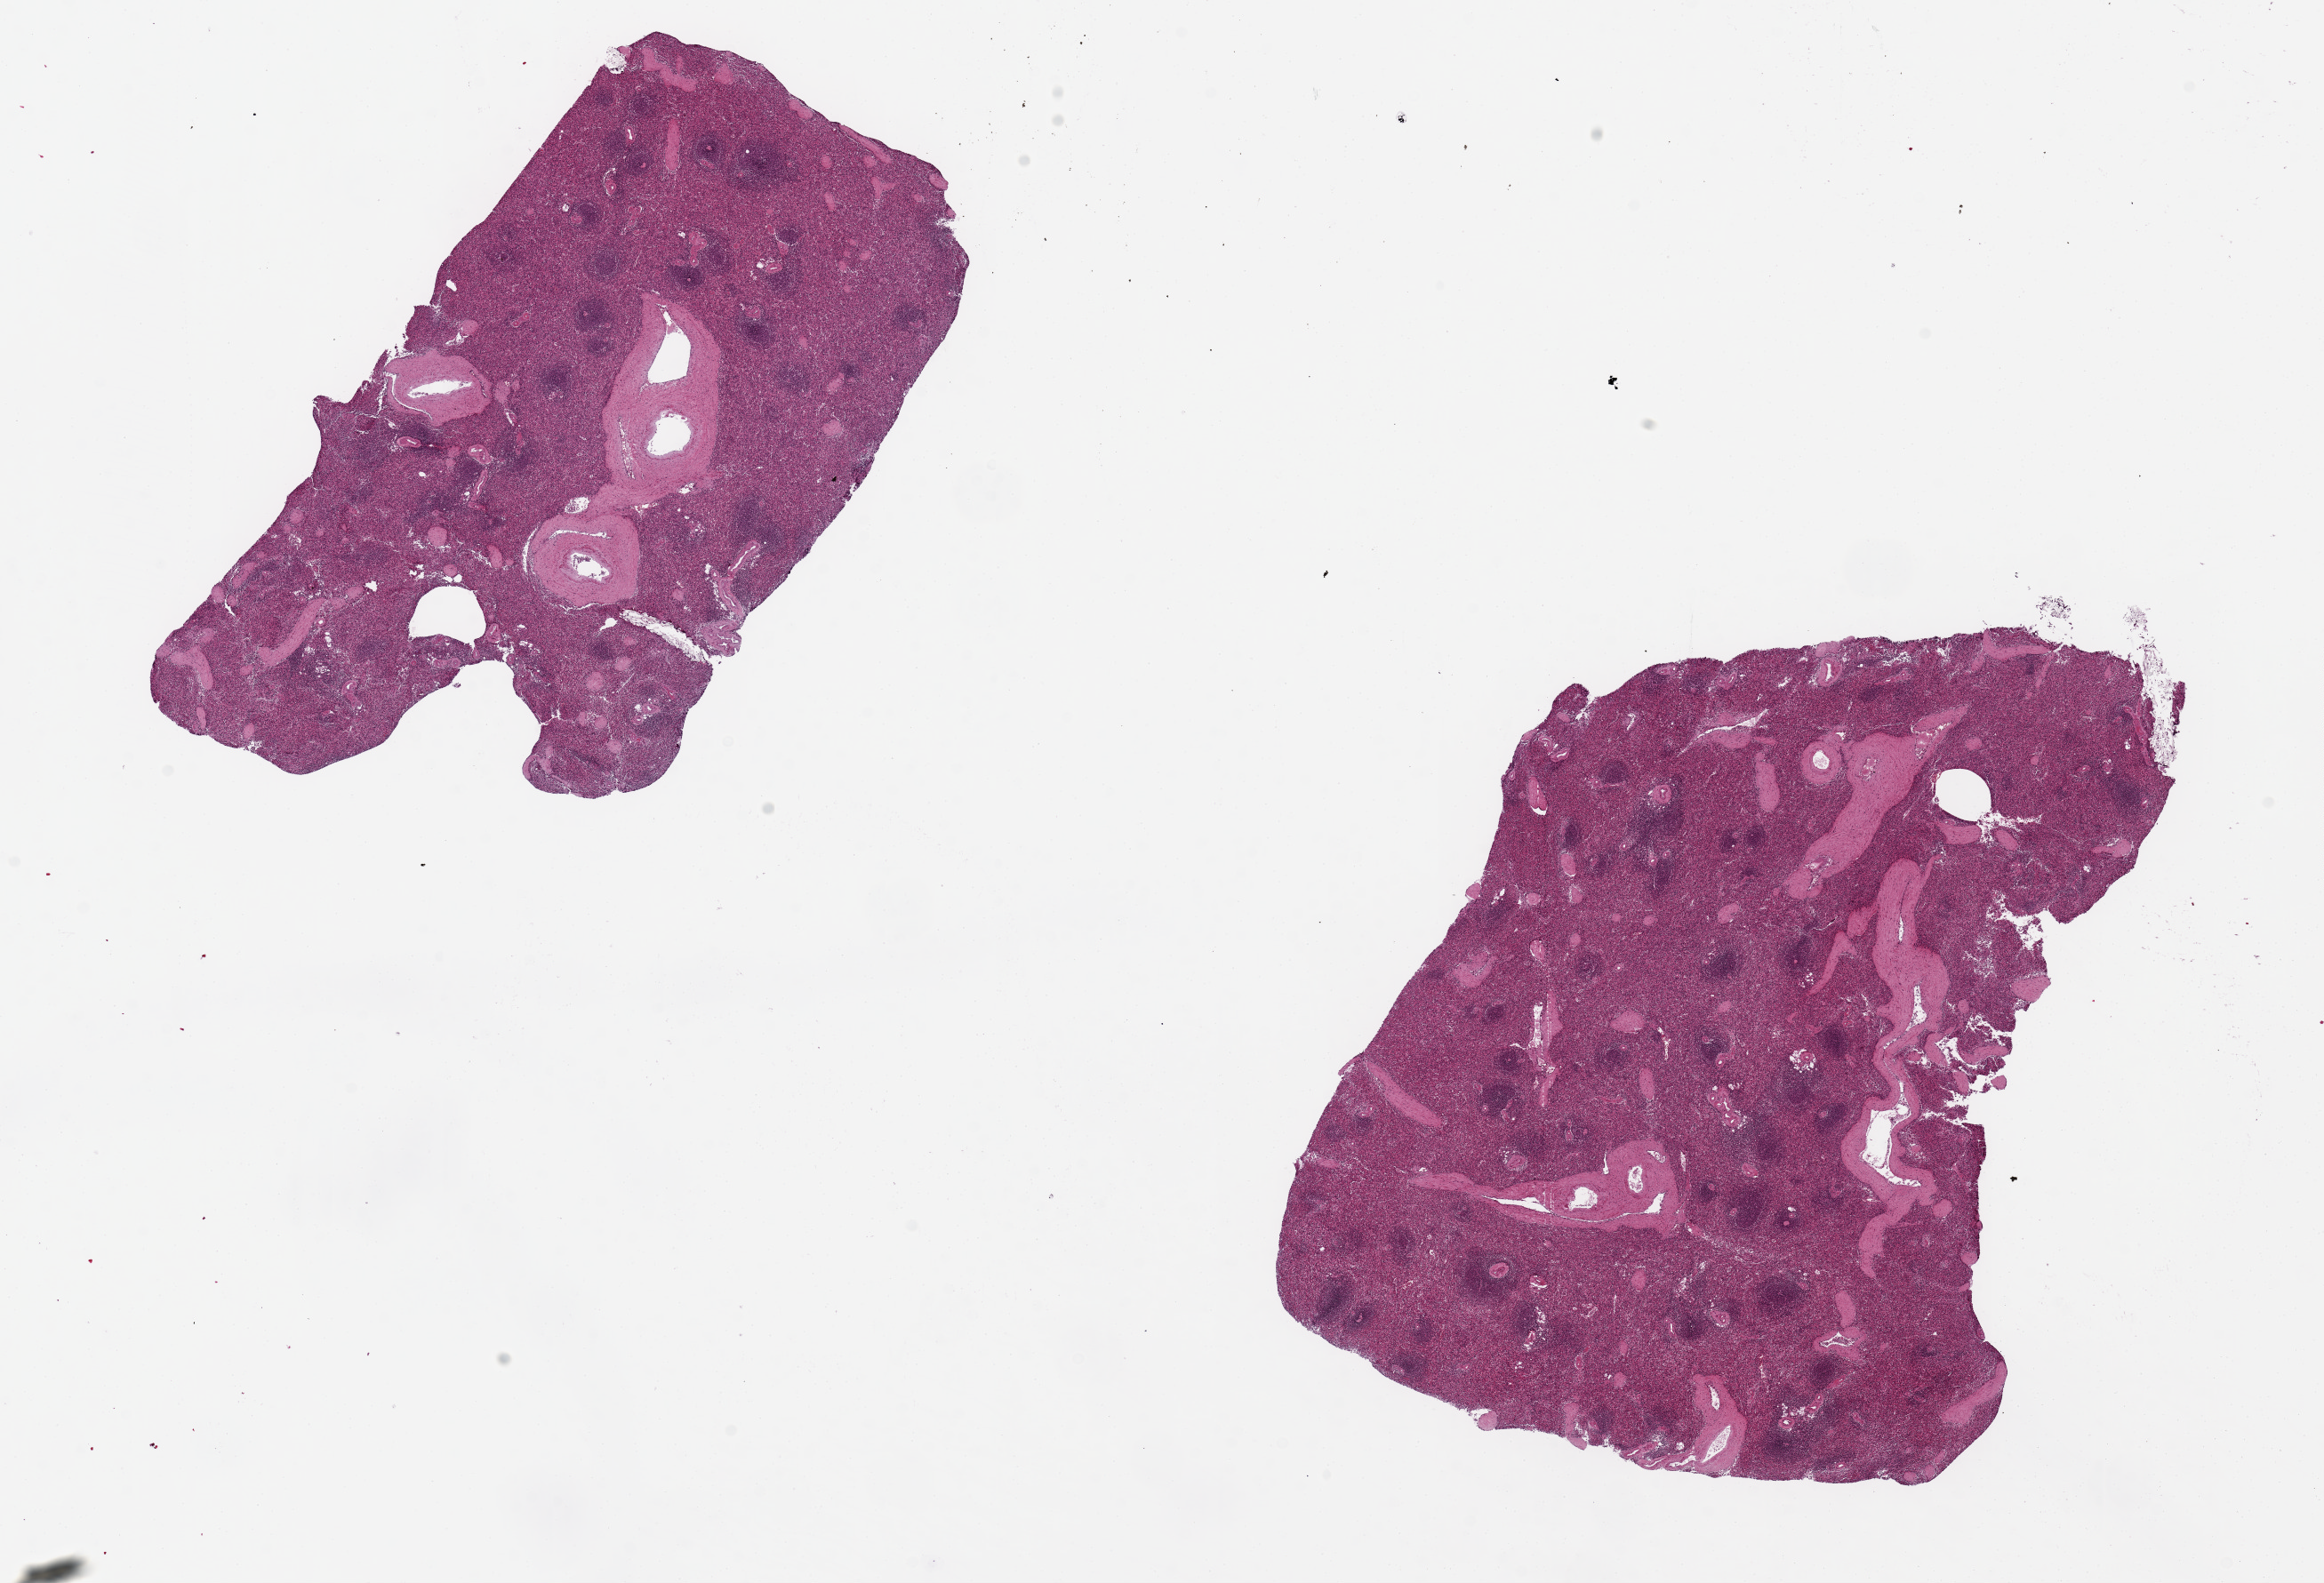
Digitized hematoxylin and eosin (H&E)-stained section — whole scanned area (about 20.7 x 14.1 mm) shown as a low-resolution overview. PAXgene-fixed, paraffin-embedded tissue. Target tissue: spleen. Donor tissue sample. Male donor.
Review note (as recorded): 2 pieces, 8x4 & 8x7mm; mild congestion.